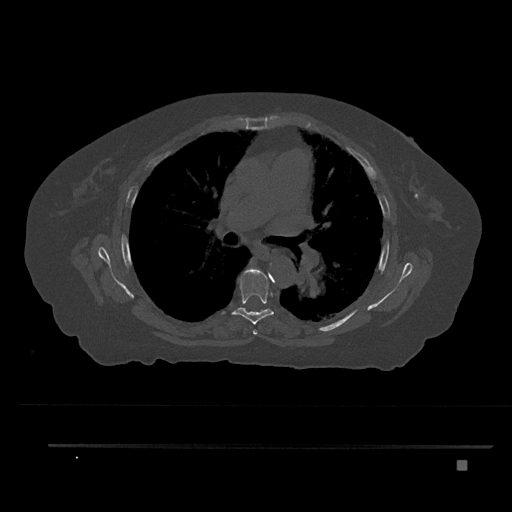
CT including the spine, one axial slice; slice 530 of 797 in the series (ordered by position); reconstruction kernel Br40s/3; 120 kVp; bone window (W 1800 / L 400 HU); 512 × 512 image matrix, field of view 437 × 437 mm. Female patient, age 76 years. From the clinical record (not read from this slice): primary cancer: lung; vertebrae with lytic lesions (as recorded): T11, L3.
Structures marked on this image (semi-automatically segmented with operator editing):
- T5 vertebra: box from (x=245, y=267) to (x=258, y=335) px
- T6 vertebra: (x=221, y=268)–(x=274, y=325)
- T7 vertebra: (x=238, y=307)–(x=240, y=309)